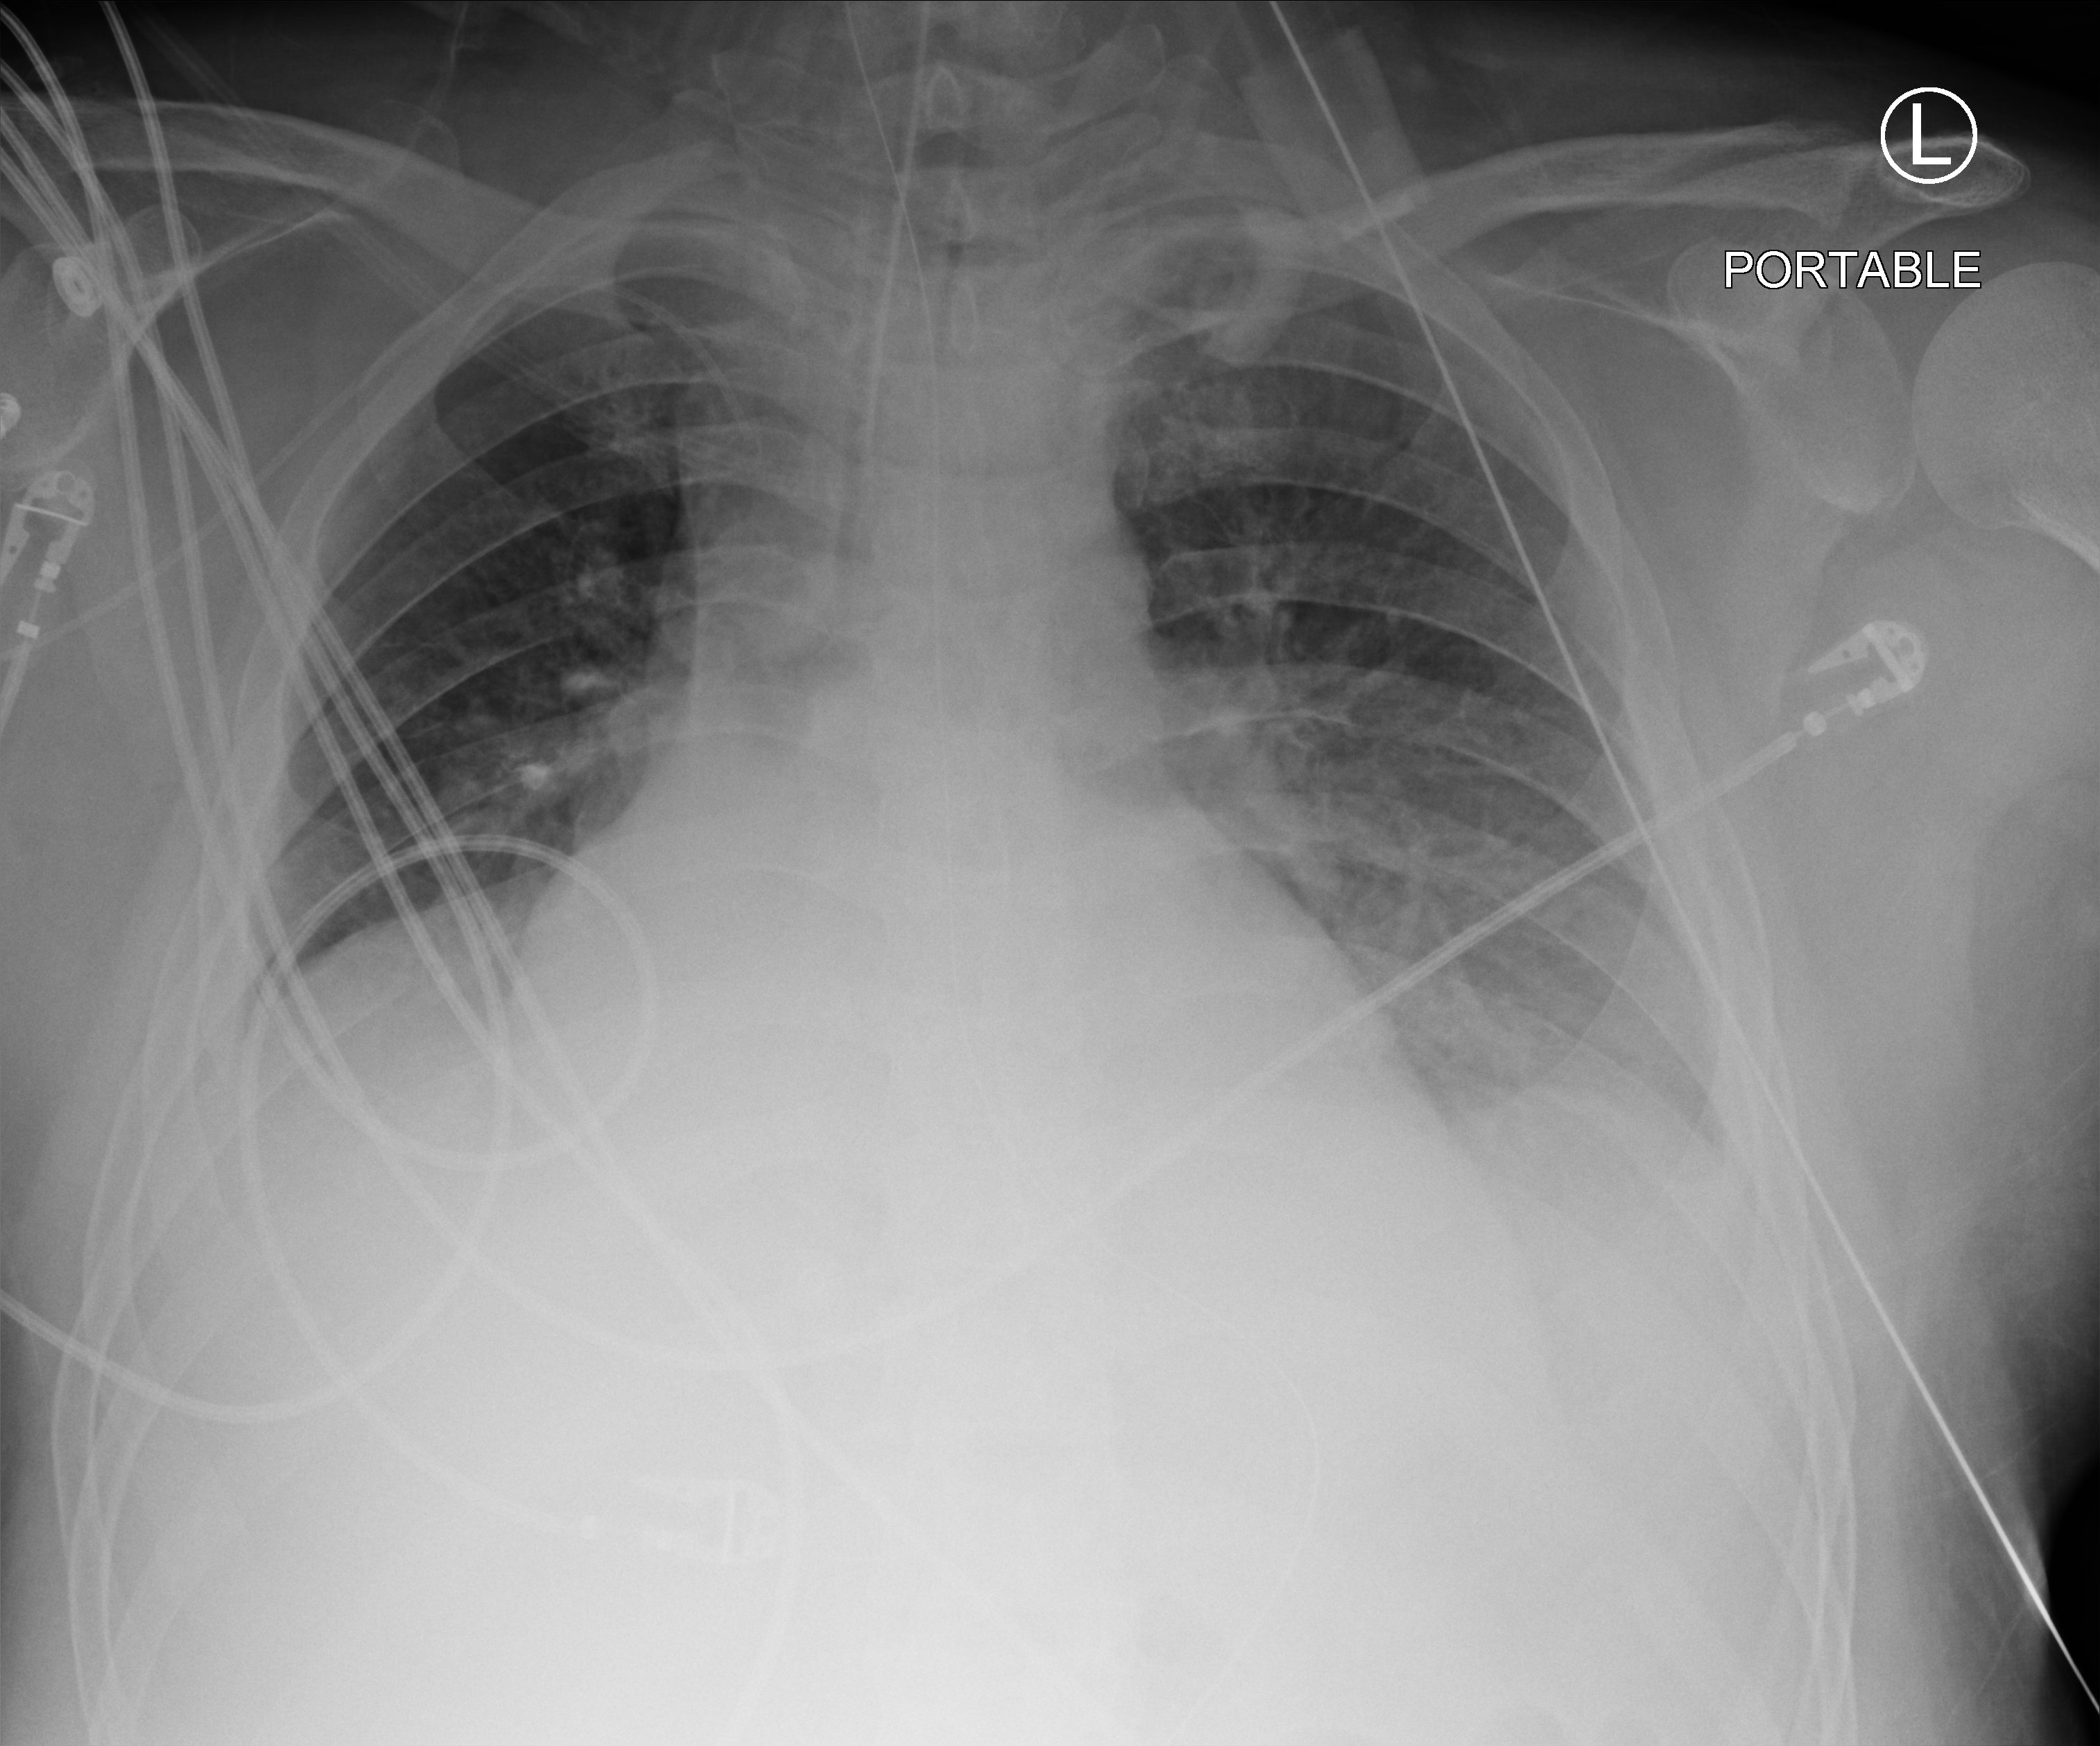
Portable chest radiograph, anteroposterior (AP) projection. Patient hospitalised with COVID-19; male, aged 18–59 years.
From the hospital-stay record, not from the radiograph (when in the stay this image was taken is not recorded):
- admitted to intensive care during this hospital stay: yes